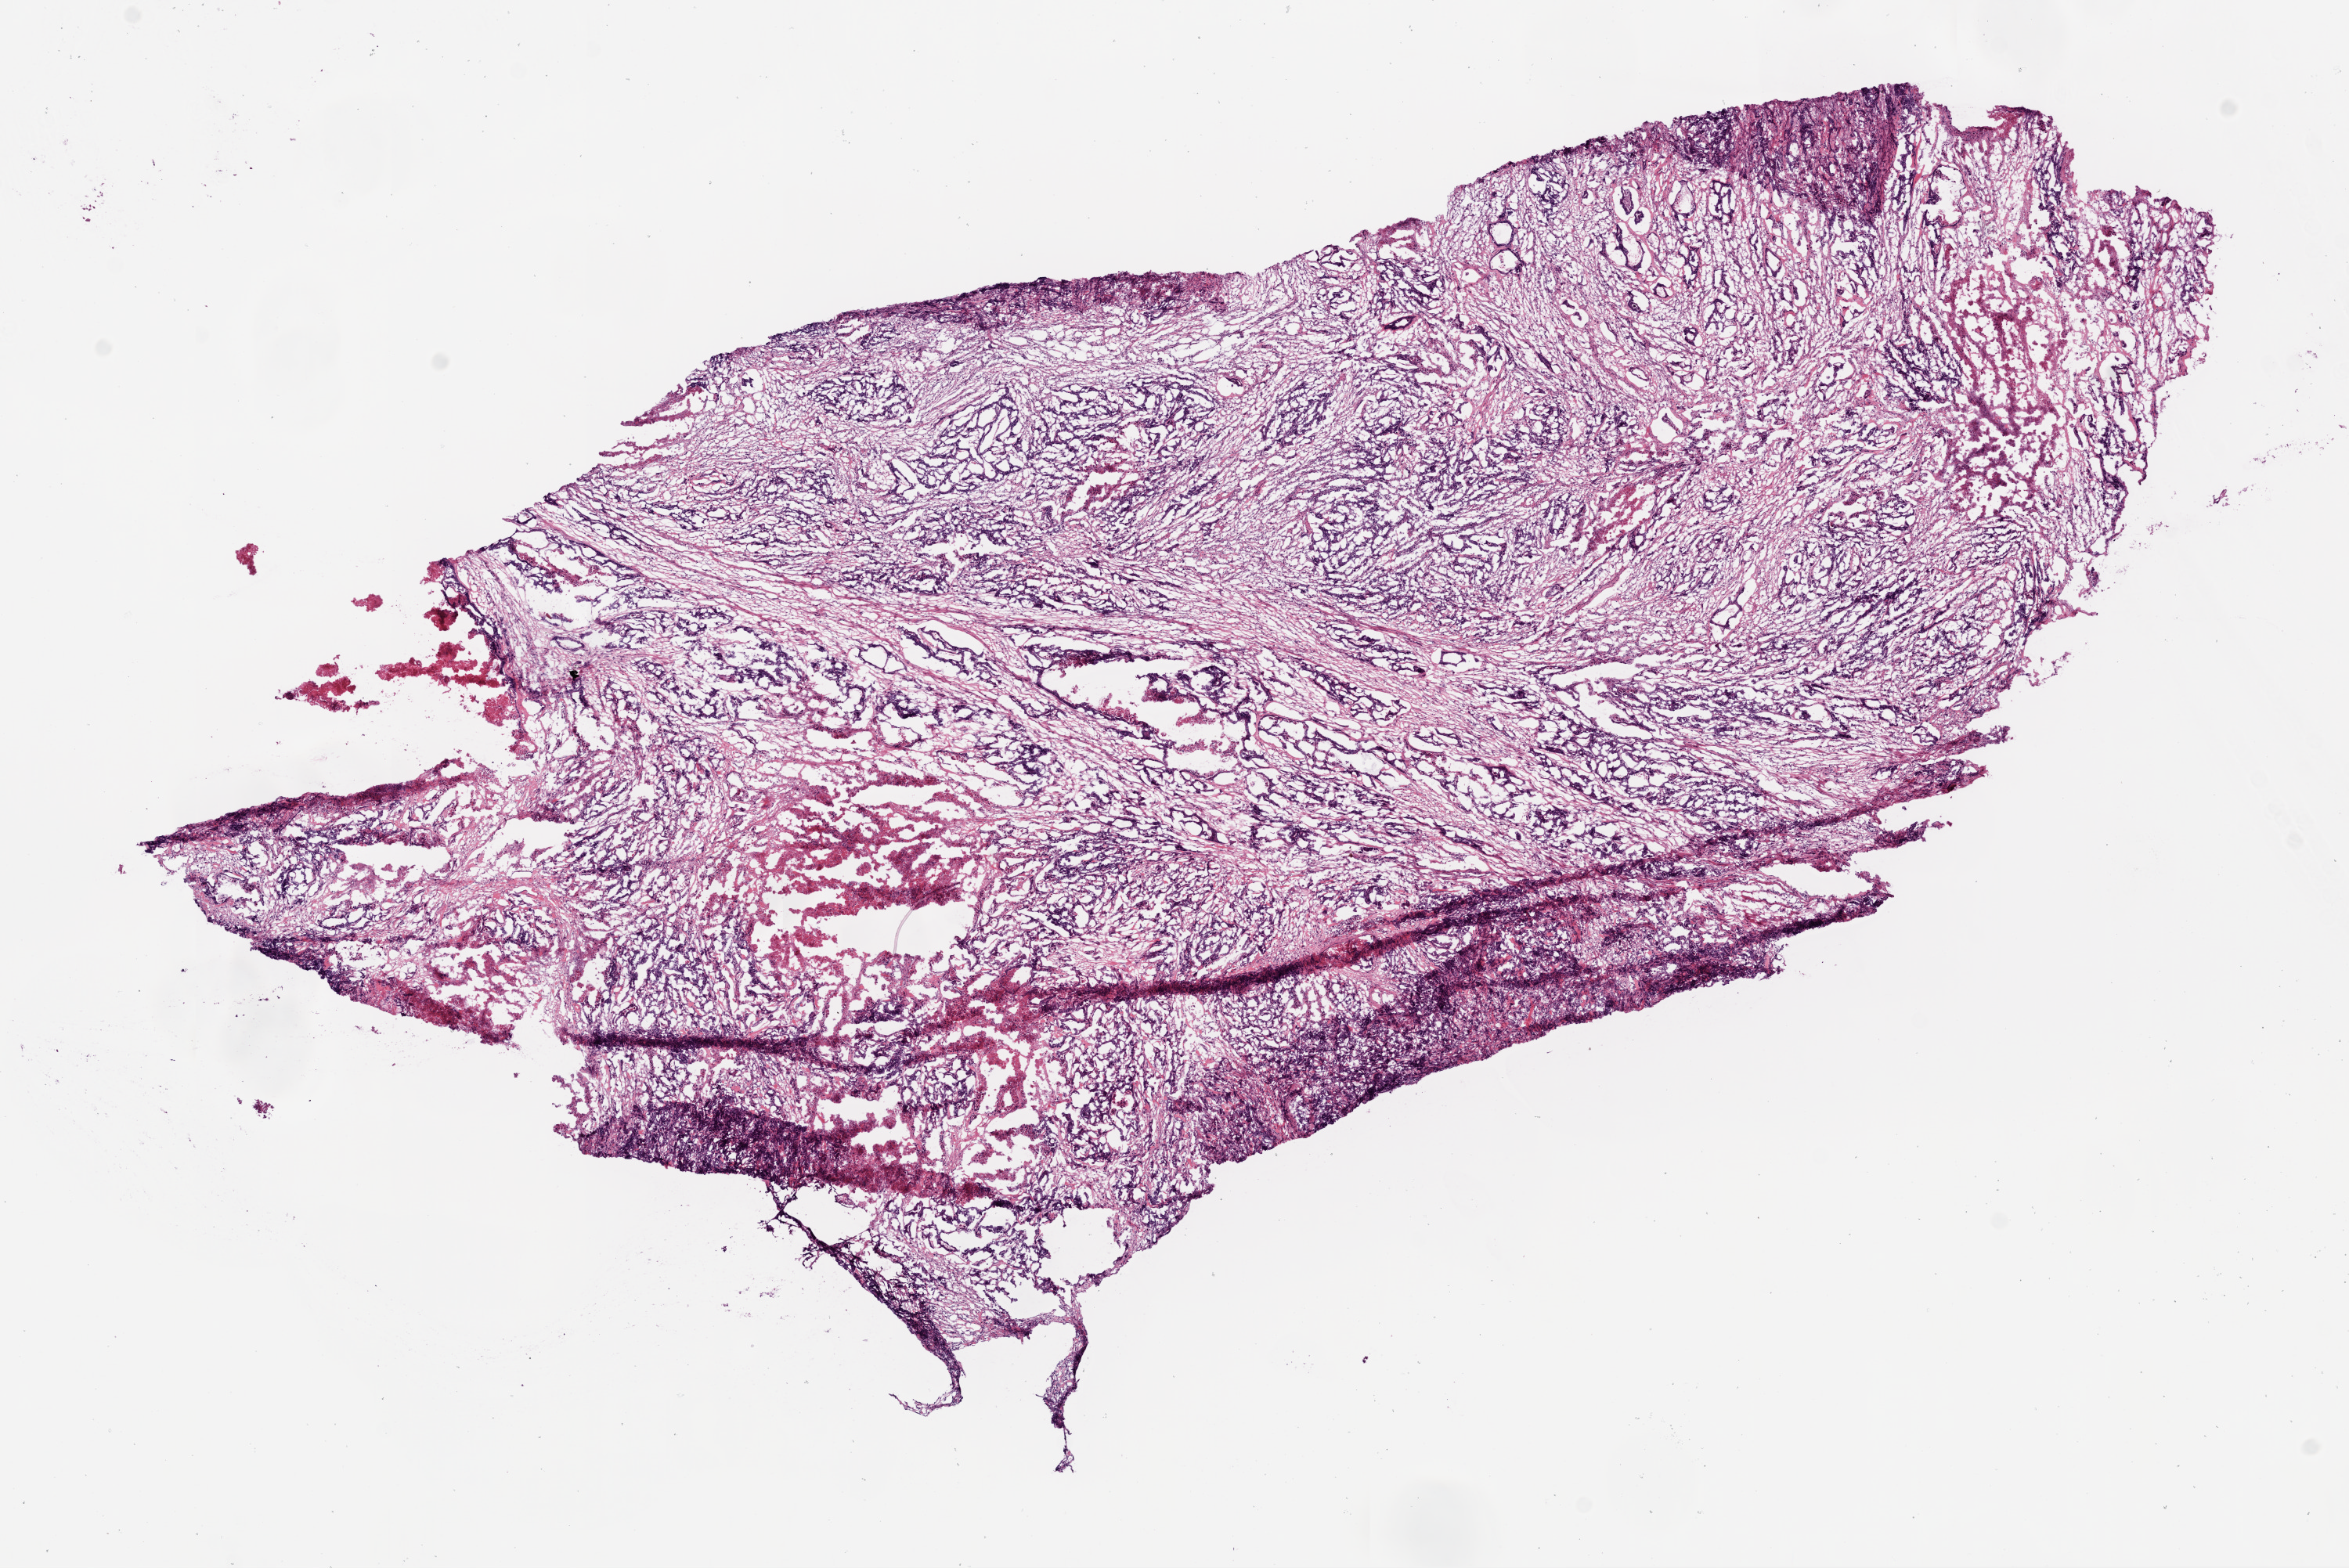
H&E-stained whole-slide image — whole scanned area (about 12.0 x 8.0 mm, slide scanned at 20x) shown as a low-resolution overview; frozen section; primary tumour sample from the colon. Patient: female, age at initial diagnosis 82 years. Composition of this section per pathologist review: tumour cells 80%, tumour nuclei 75%.
Histologic diagnosis: Adenocarcinoma, NOS (cecum).